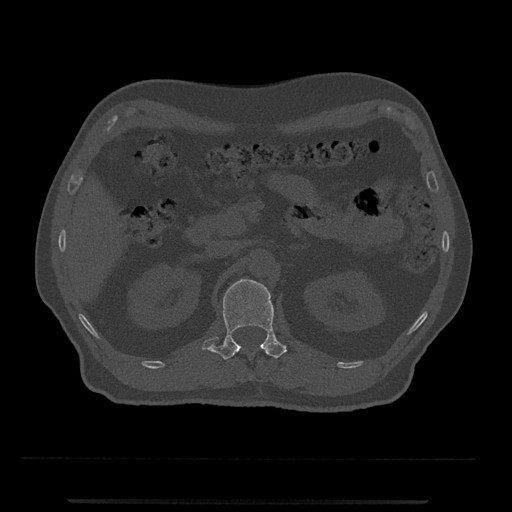
CT including the spine, one axial slice. Slice 346 of 797 in the series (ordered by position). Reconstruction kernel Br40s/3. Bone window (W 1800 / L 400 HU). 512 × 512 image matrix, field of view 419 × 419 mm. Male patient, age 63 years. From the clinical record (not read from this slice): primary cancer: prostate.
Annotated regions visible in this slice (semi-automatic segmentation, software-assisted and operator-edited):
- L1 vertebra: bounding box <202,279,293,360> (left, top, right, bottom; pixels)